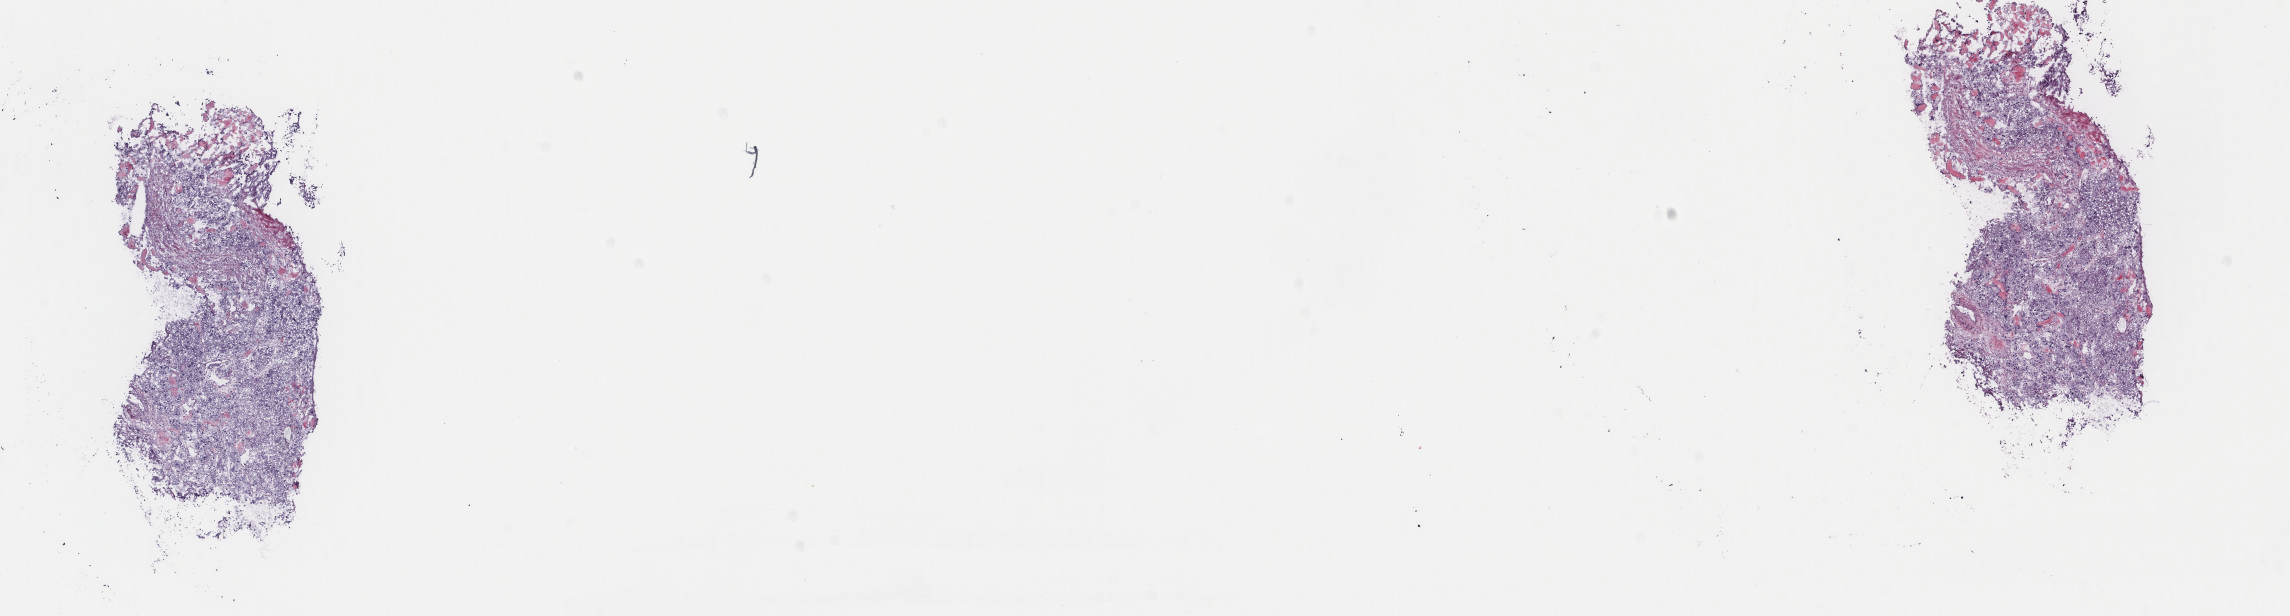
Hematoxylin and eosin (H&E) stained whole-slide image, whole scanned area (about 18.2 x 4.9 mm) shown as a low-resolution overview, frozen section from the top of the tissue portion, sample: primary tumour, adrenal gland. Patient: female, age at initial diagnosis 57 years. Slide review estimates, as recorded: tumour cells 85%, tumour nuclei 100%, normal cells 0%, stromal cells 15%, necrosis 0%. Infiltration values recorded for this section: lymphocyte infiltration 1%, monocyte infiltration 1%, neutrophil infiltration 0%.
Lymph nodes positive (case pathology): 0 of 1 examined. Histologic diagnosis: Pheochromocytoma, malignant.